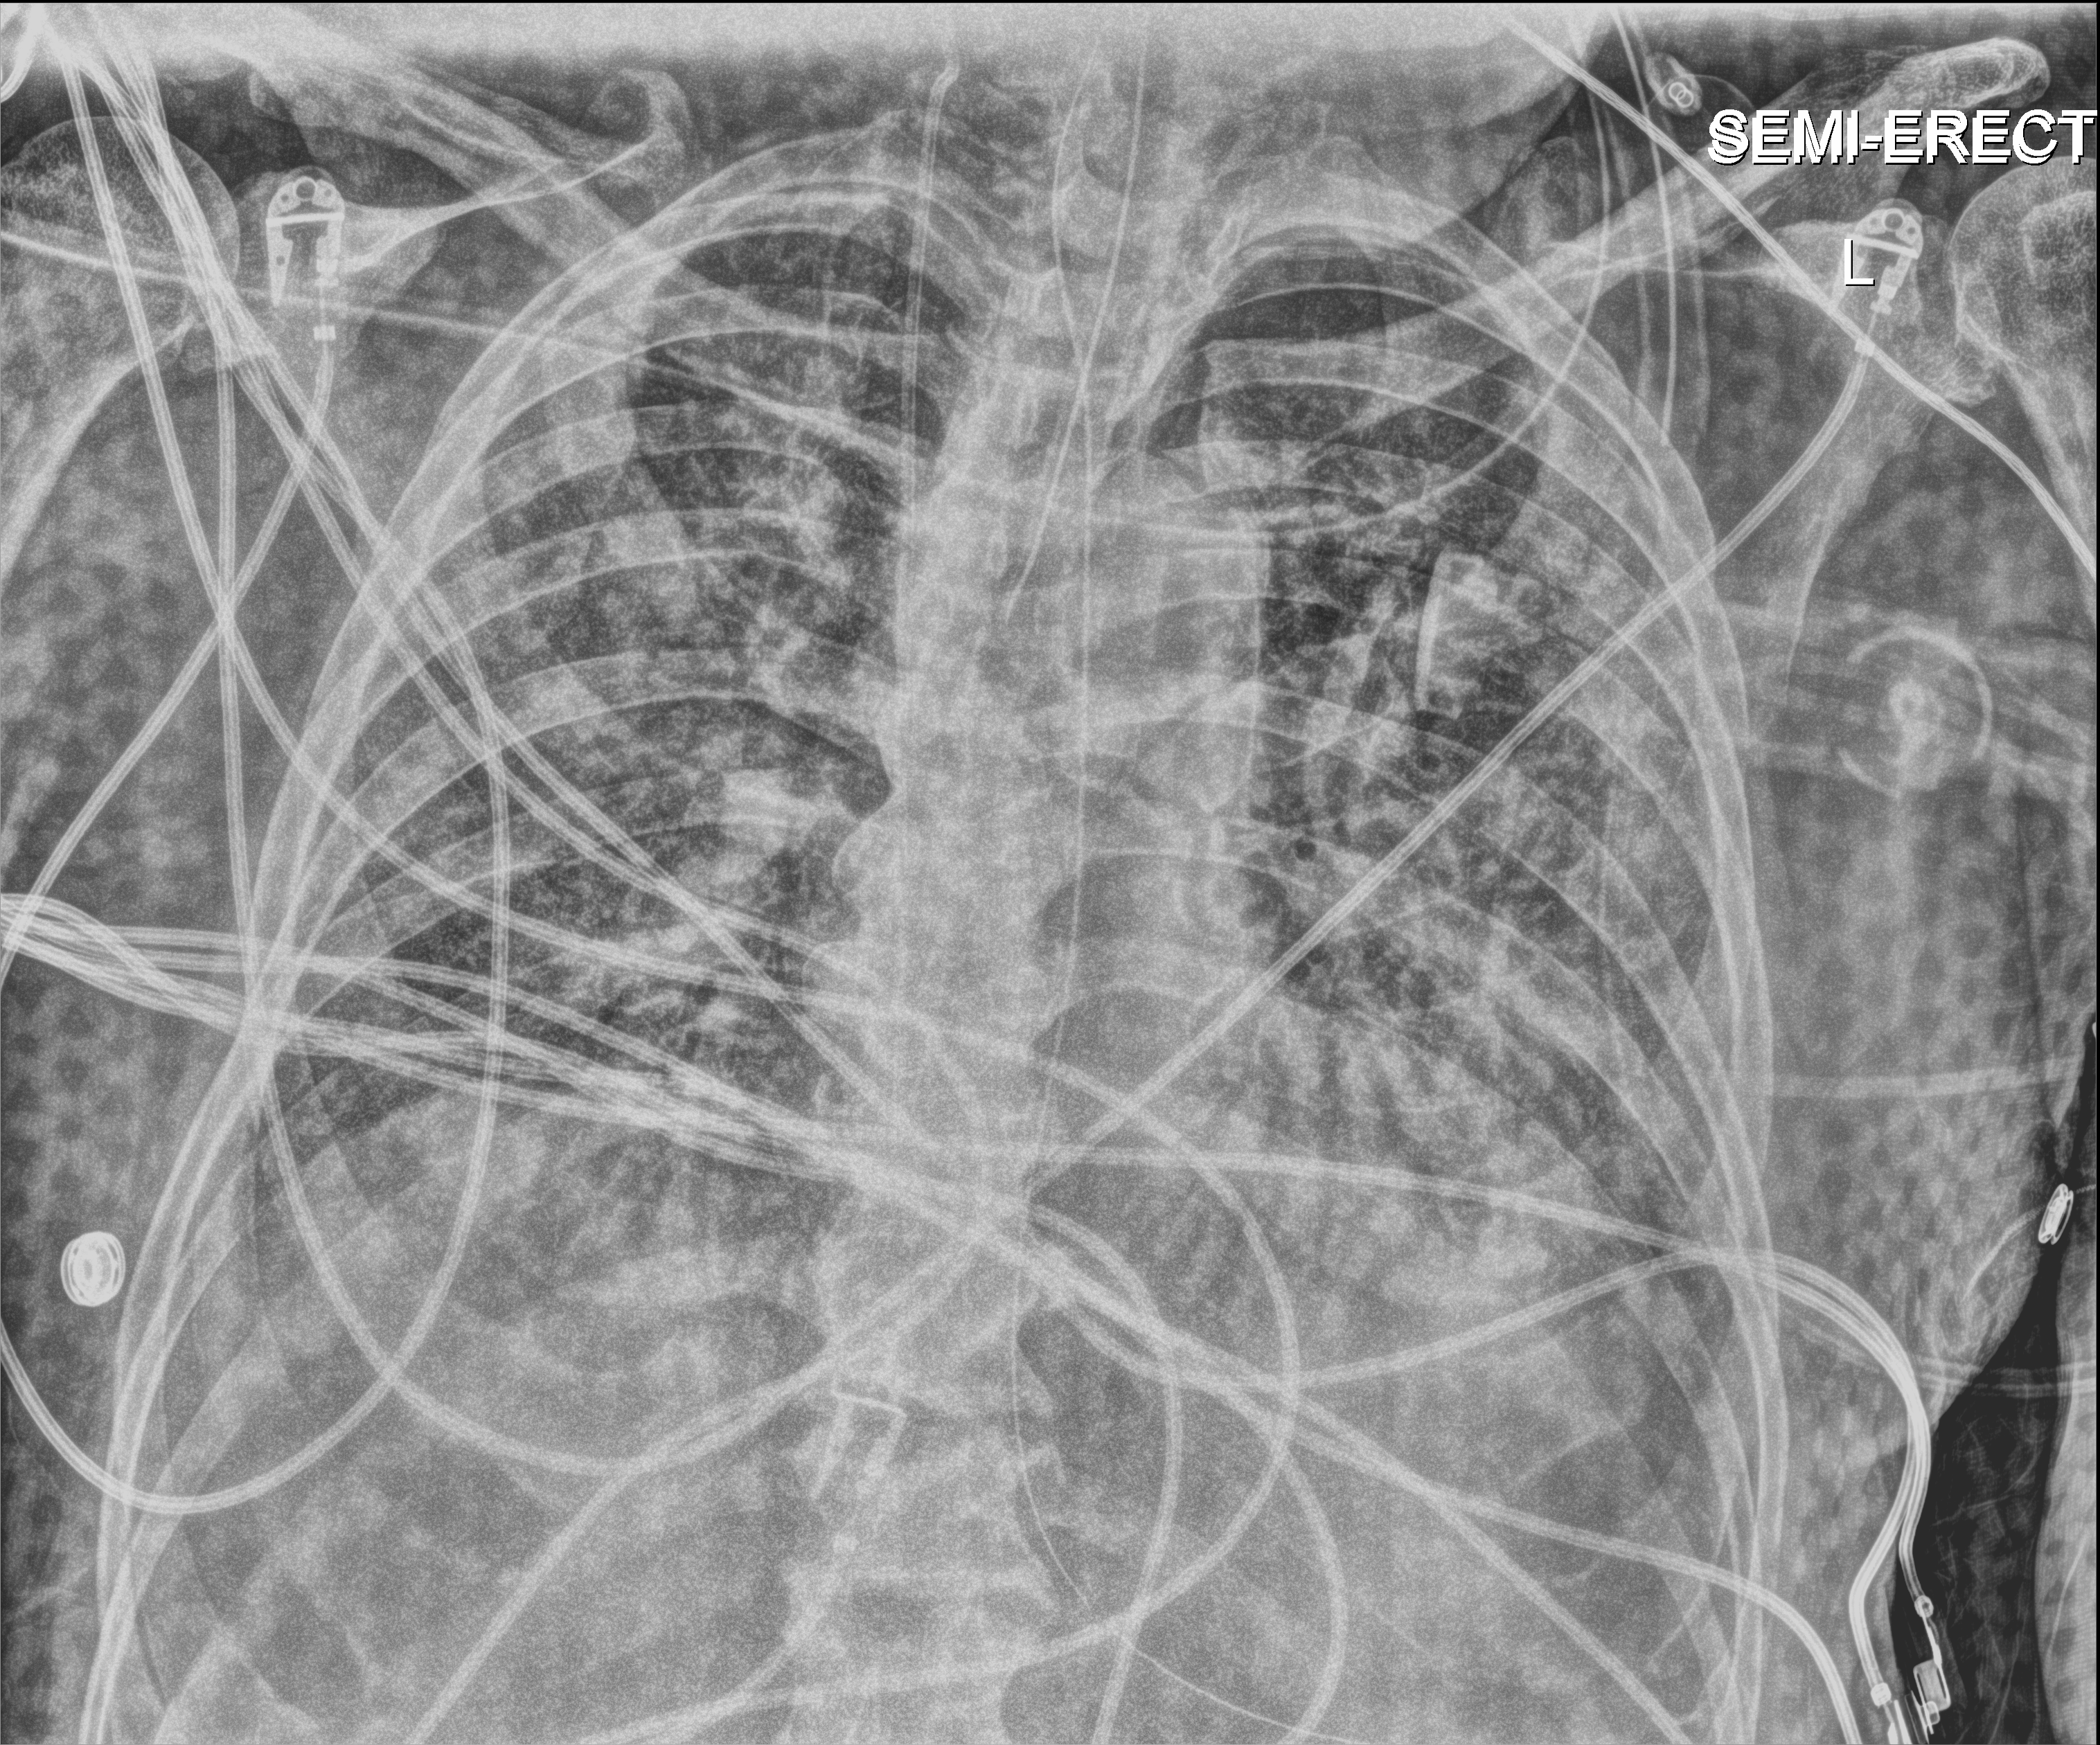
Portable chest radiograph; anteroposterior (AP) projection. Male patient hospitalised with COVID-19, age 75–90 years.
Admission-level facts for this patient (not findings on this image; timing relative to this image not recorded):
- mechanically ventilated during this hospital stay: yes